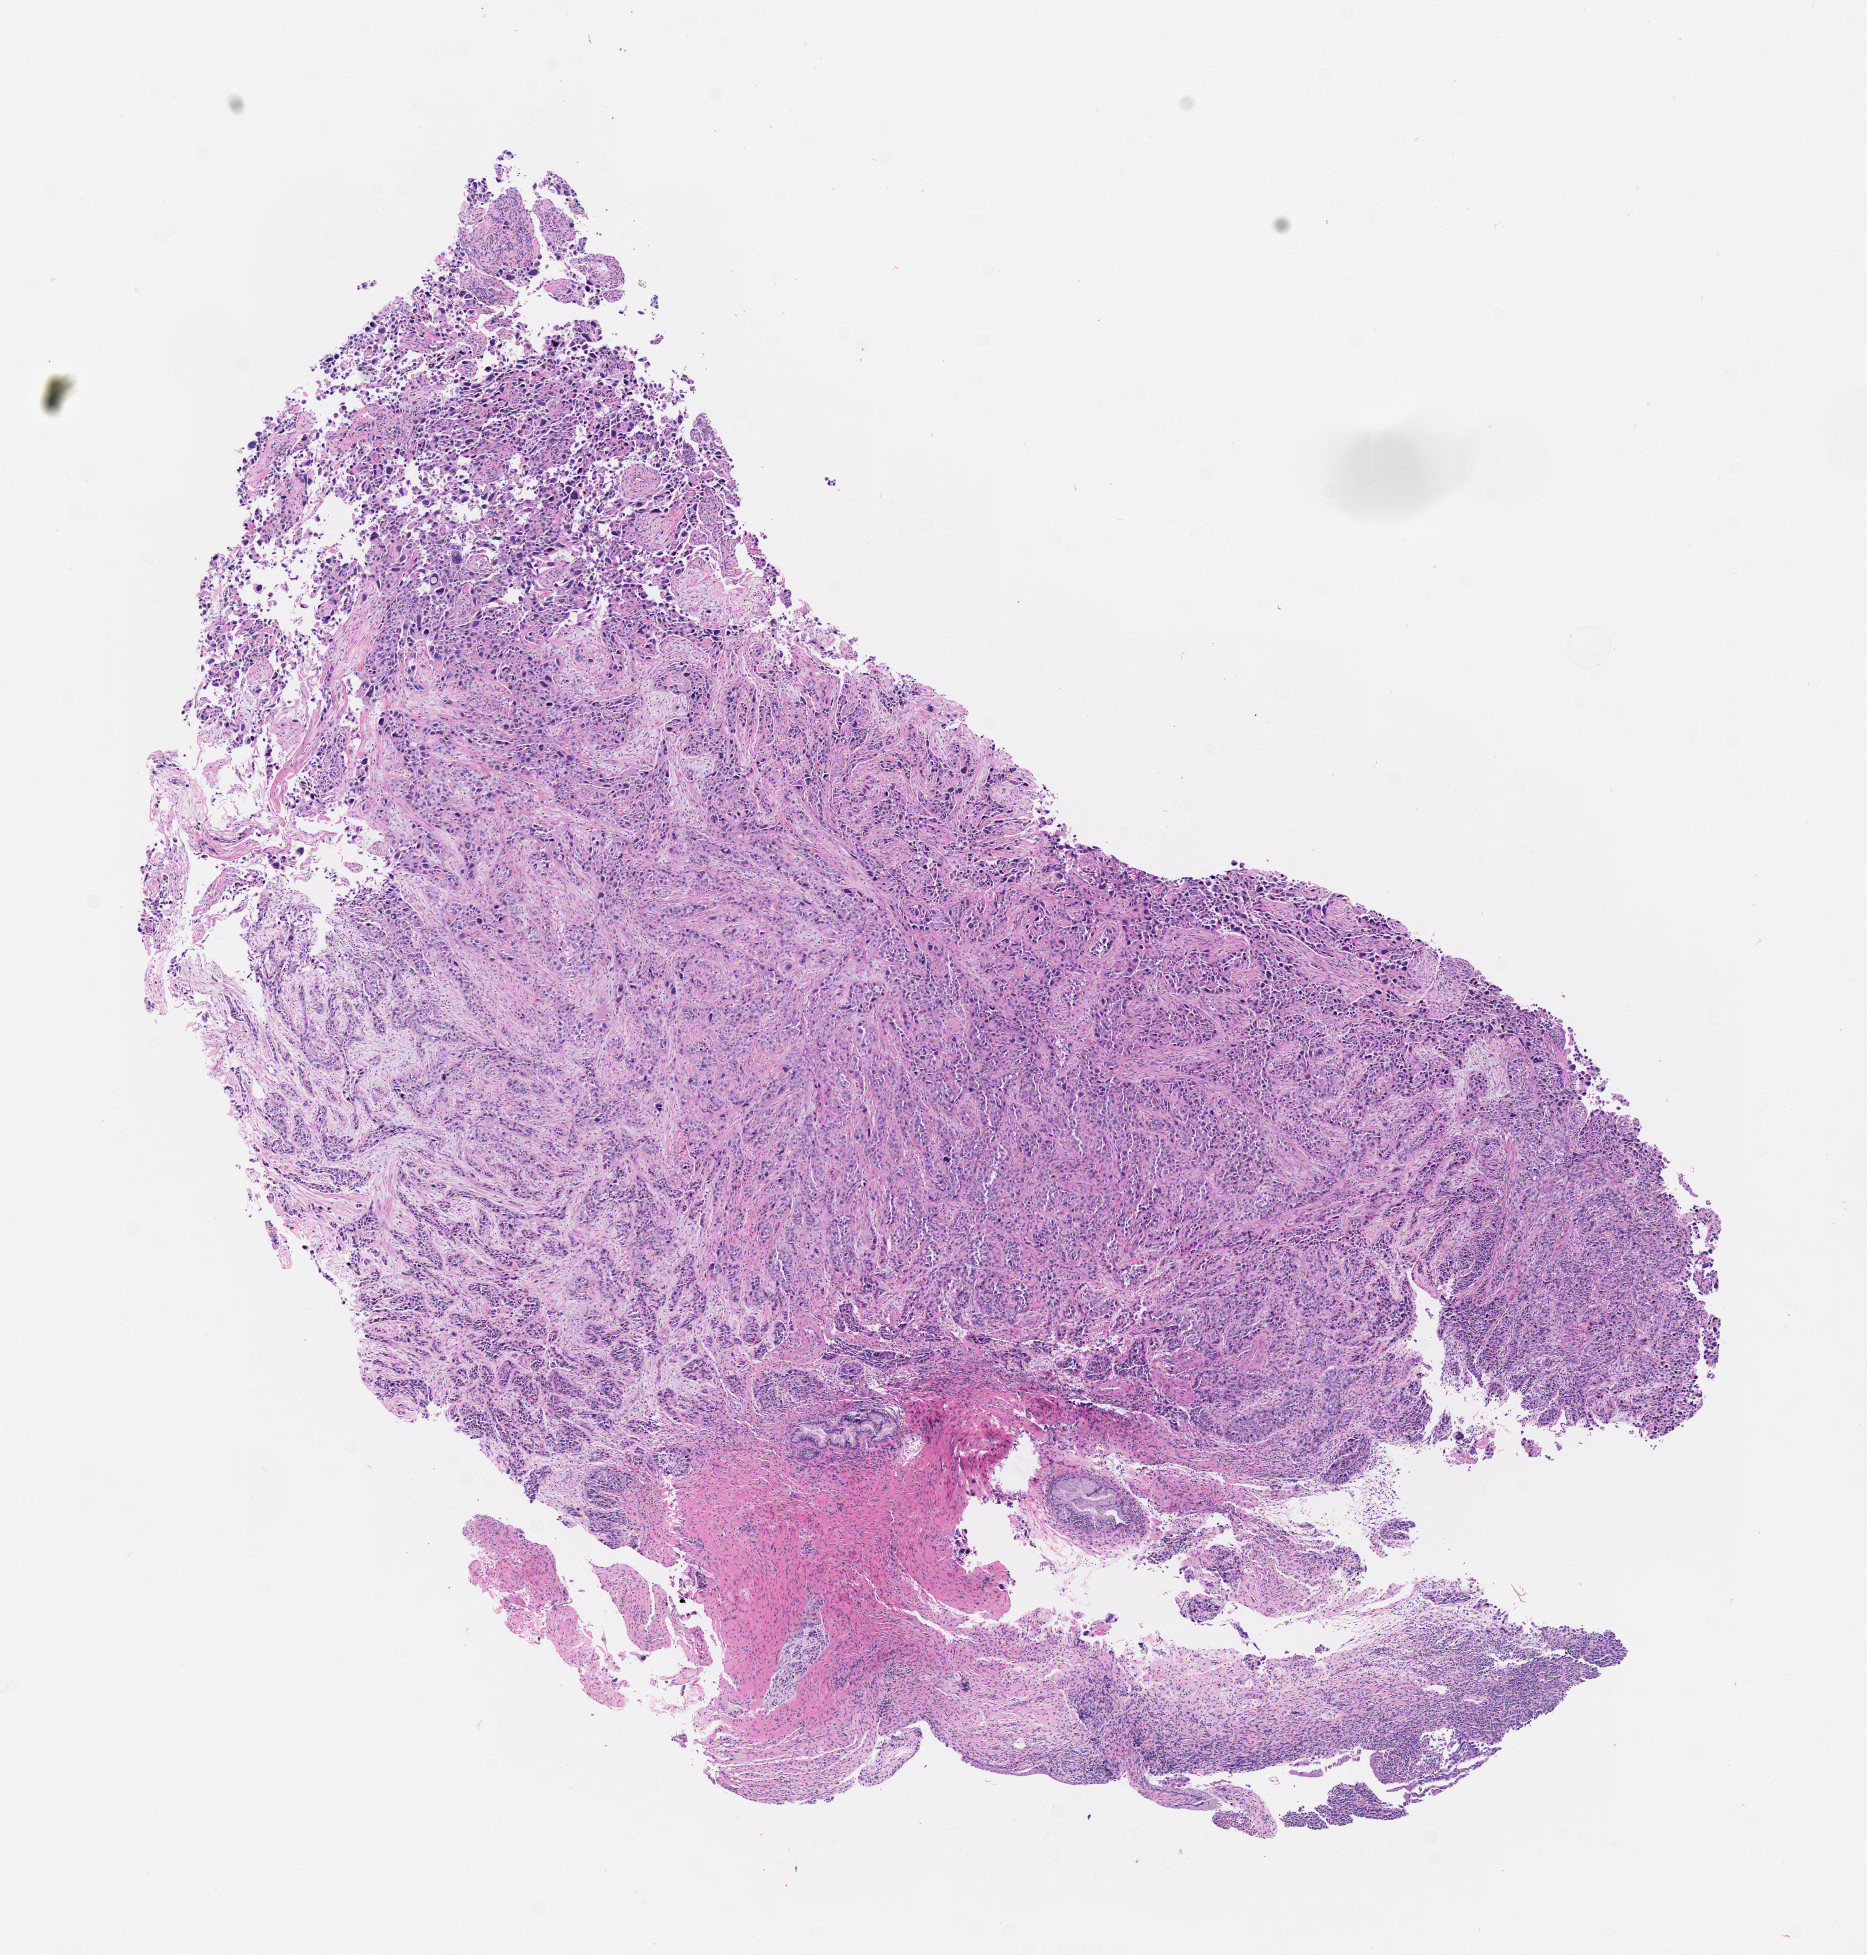
Digitized haematoxylin and eosin-stained section — whole scanned area (about 7.5 x 7.9 mm) shown as a low-resolution overview. Tumor tissue. Site: cervix. Female patient, age 38 years.
- histologic diagnosis: Squamous cell carcinoma, large cell, nonkeratinizing, NOS